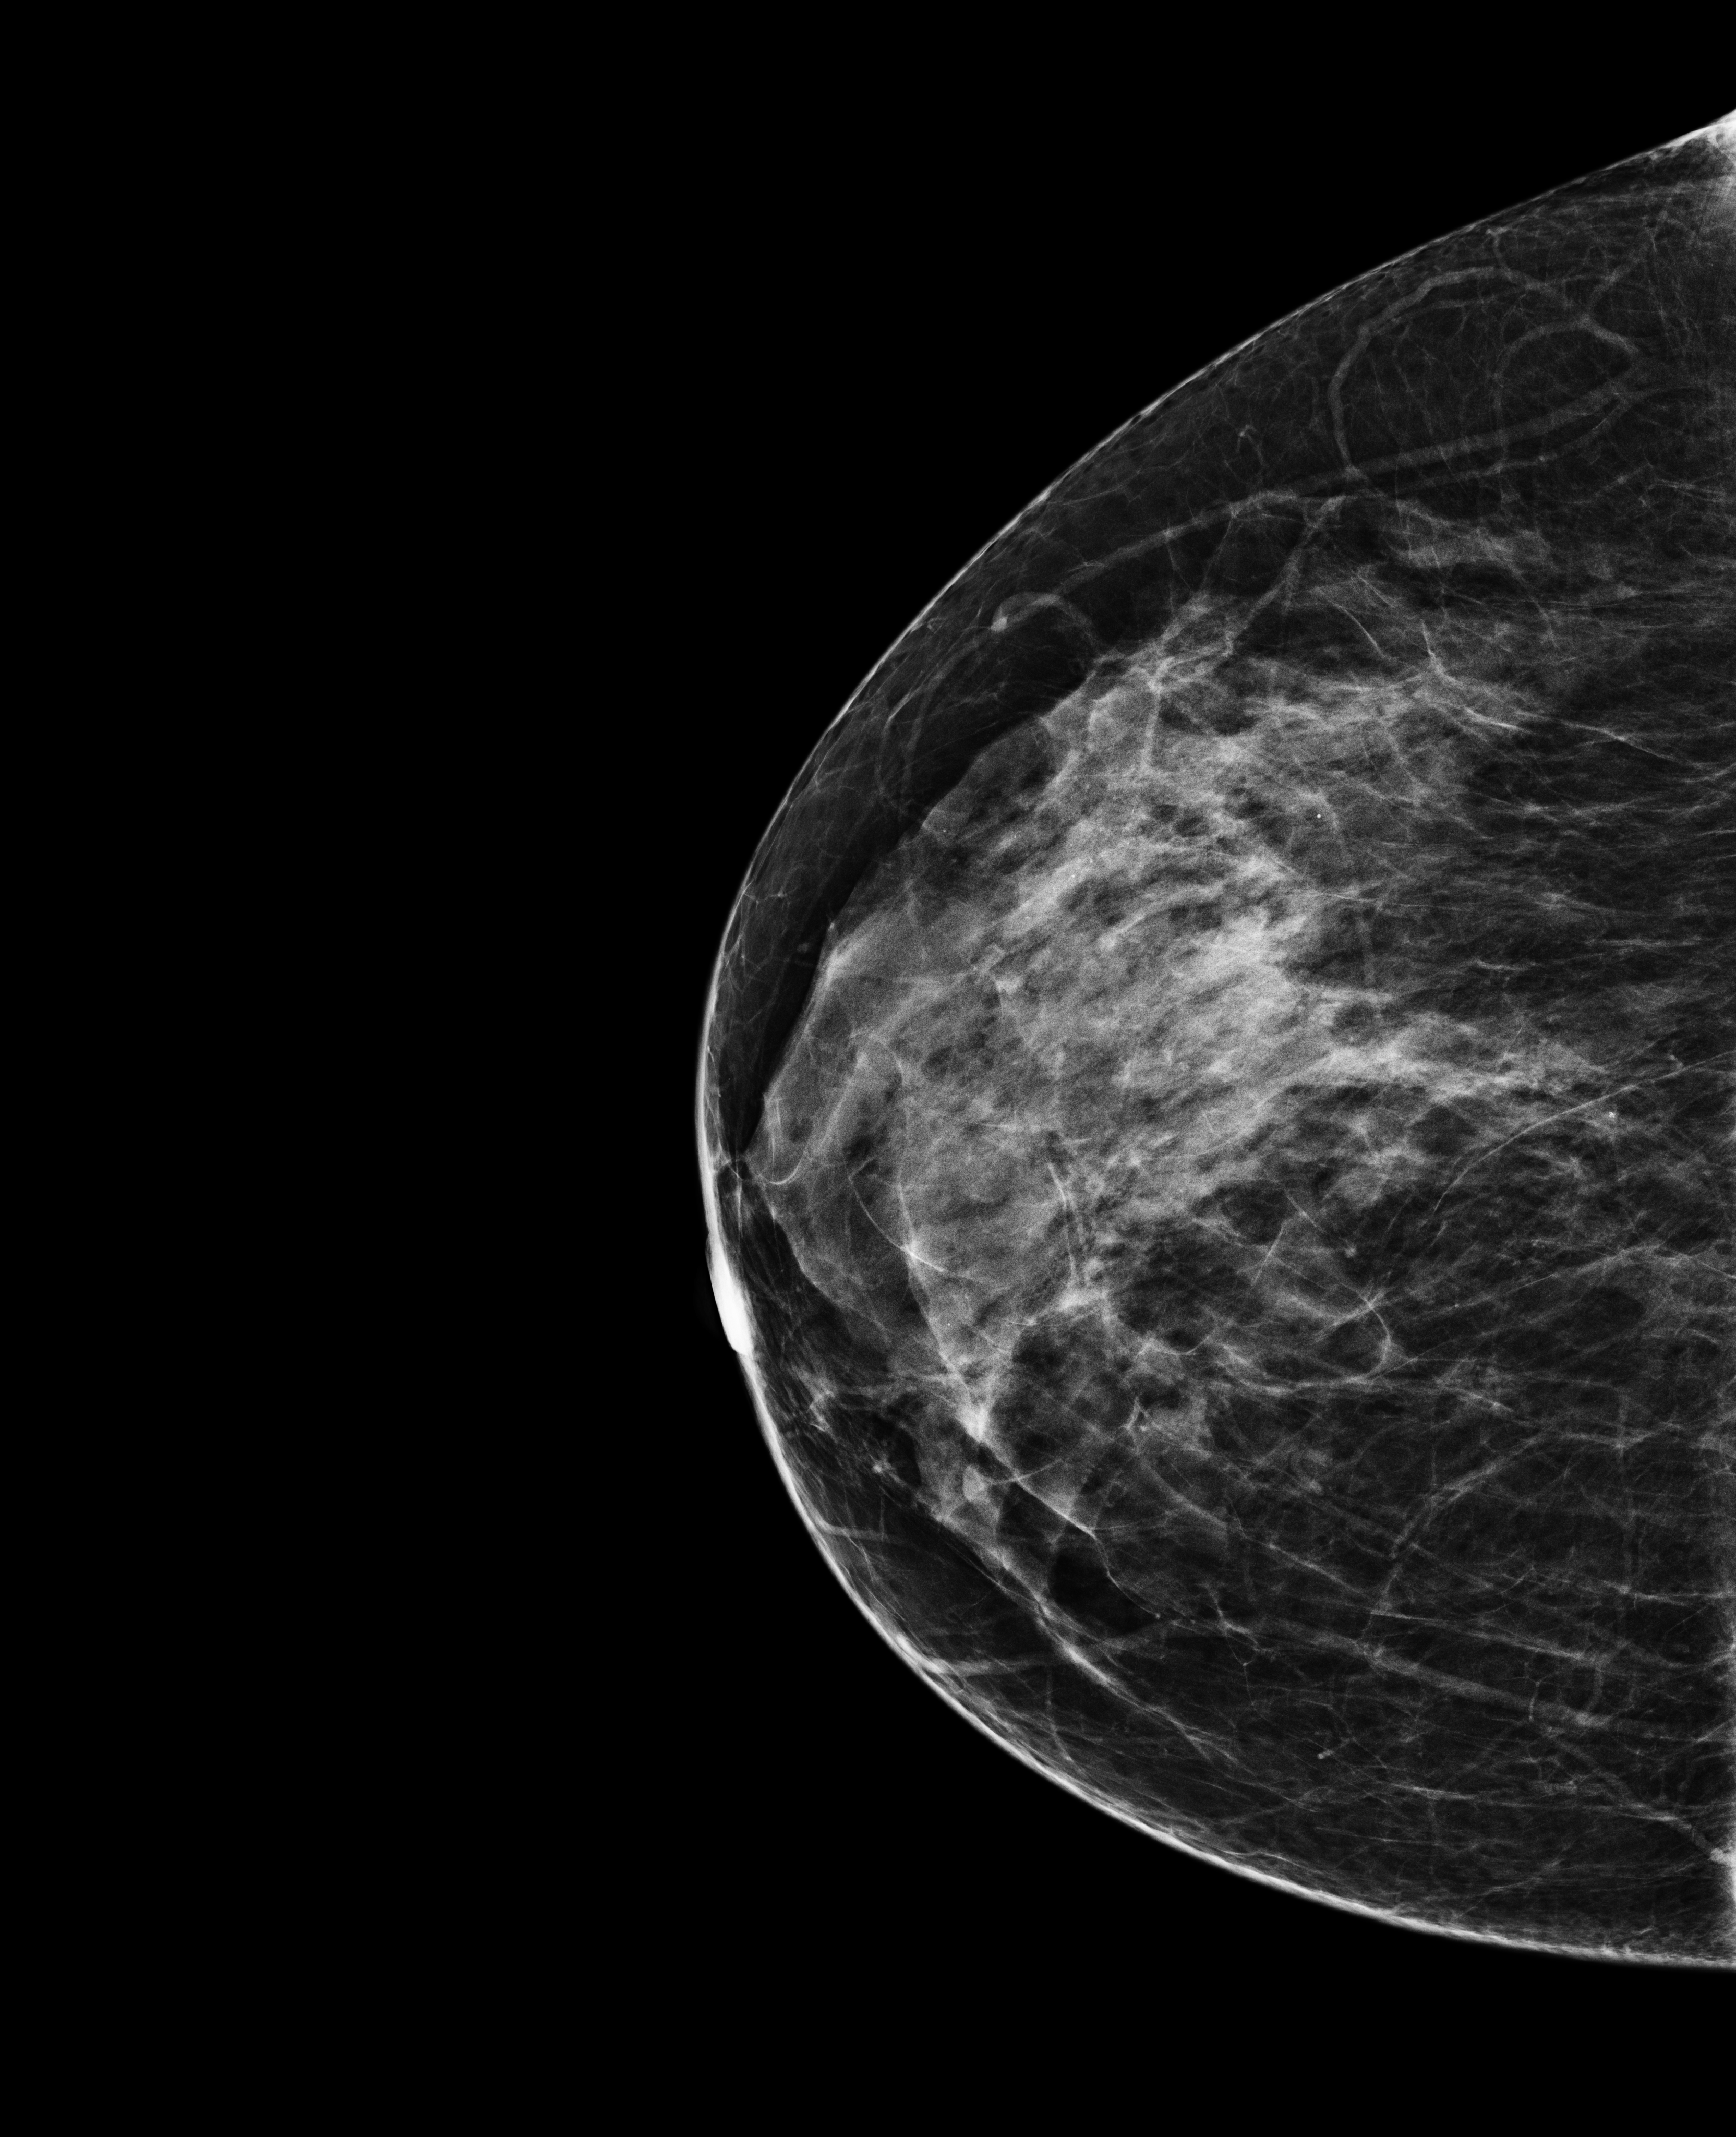
Full-field digital mammogram (FFDM); right breast; cranio-caudal projection; annual screening mammography examination; system: Selenia Dimensions. Patient: female, 48 years.
Final BI-RADS assessment for this screening round (tomosynthesis exam, both breasts): category 2.